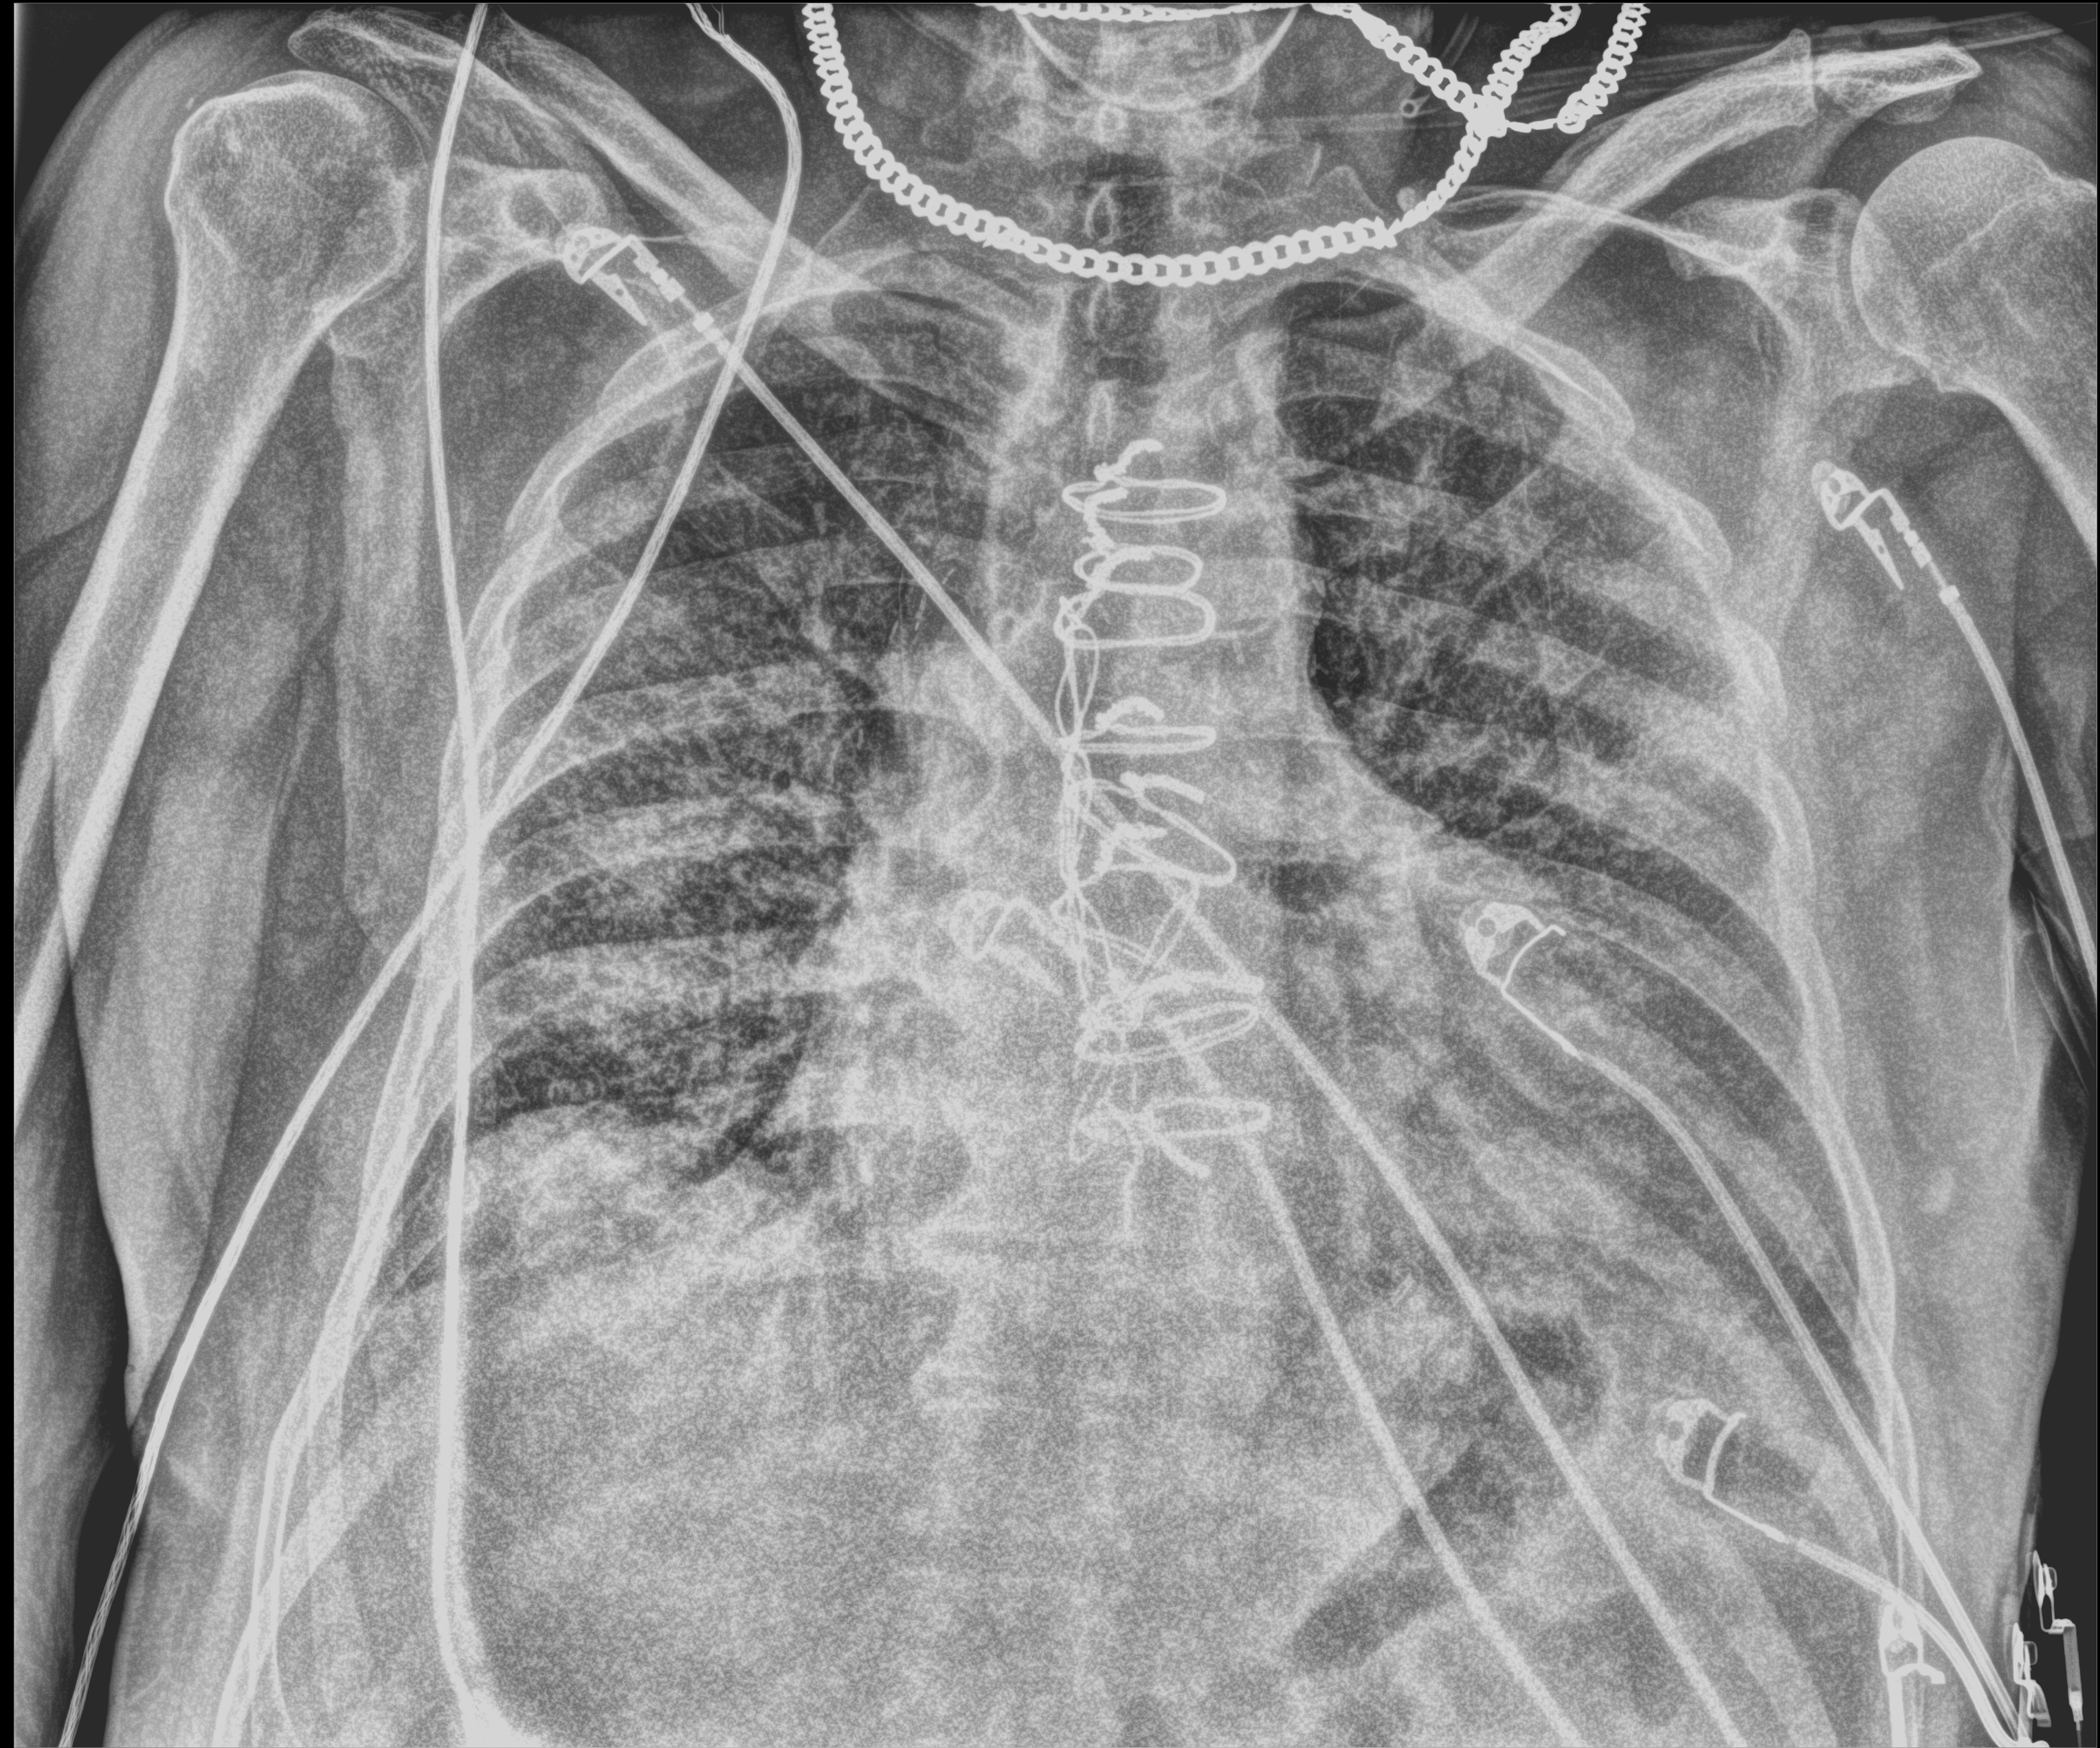
Portable chest radiograph. Patient hospitalised with COVID-19; male, aged 75–90 years.
Admission-level facts for this patient (not findings on this image; timing relative to this image not recorded):
- admitted to intensive care during this hospital stay: no
- mechanically ventilated during this hospital stay: yes